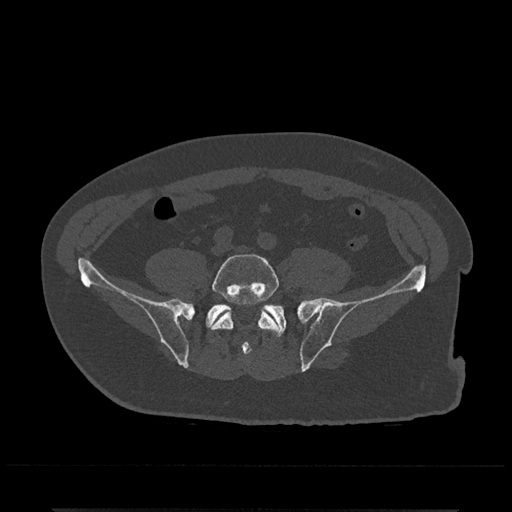
CT including the spine, one axial slice; reconstruction kernel Br40s/3; bone window (W 1800 / L 400 HU); 512 × 512 image matrix, field of view 393 × 393 mm. Male patient, age 67 years. Case-level facts recorded for this patient, not image findings: primary cancer: prostate.
Annotated regions visible in this slice (semi-automatically segmented with operator editing):
- L5 vertebra: box from (x=210, y=254) to (x=279, y=353) px